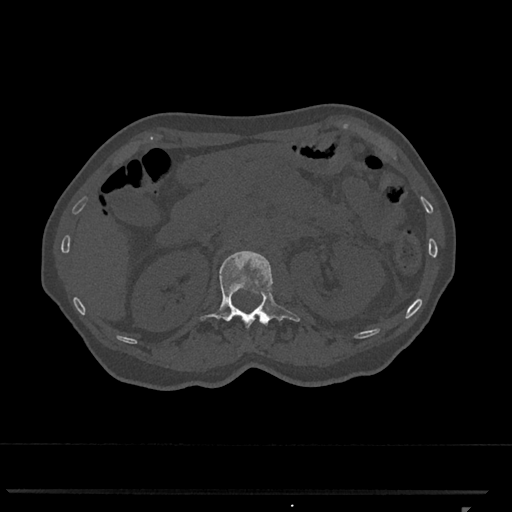
CT including the spine, one axial slice; slice 406 of 793 in the series (ordered by position); reconstruction kernel Br40s/3; 120 kVp; bone window (W 1800 / L 400 HU); 0.5 mm slice thickness; 512 × 512 image matrix, field of view 380 × 380 mm. Patient: female, 62 years. From the clinical record (not read from this slice): primary cancer: renal.
Structures marked on this image (semi-automatic segmentation, software-assisted and operator-edited):
- L1 vertebra: bounding box <200,251,300,329> (left, top, right, bottom; pixels)